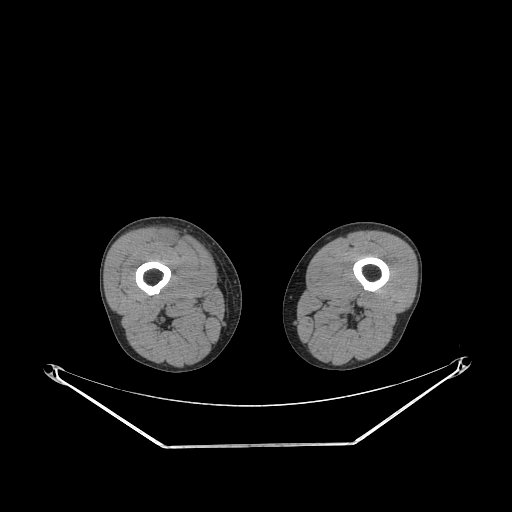
CT of an extremity soft-tissue mass (from a PET/CT study), one axial slice; slice 228 of 311 in the series (ordered by position); 140 kVp; soft-tissue window (W 400 / L 40 HU); 3.75 mm slice thickness; 512 × 512 image matrix, field of view 500 × 500 mm. Male patient. From the clinical record (not read from this slice): histological type: pleiomorphic leiomyosarcoma; grade: intermediate; site of the primary tumour: right thigh.
Annotated regions visible in this slice (expert contour drawn on MRI and transferred to this co-registered scan by the dataset authors):
- gross tumour volume including surrounding oedema: bounding box (x1, y1, x2, y2) in pixels: (160, 231, 184, 247)